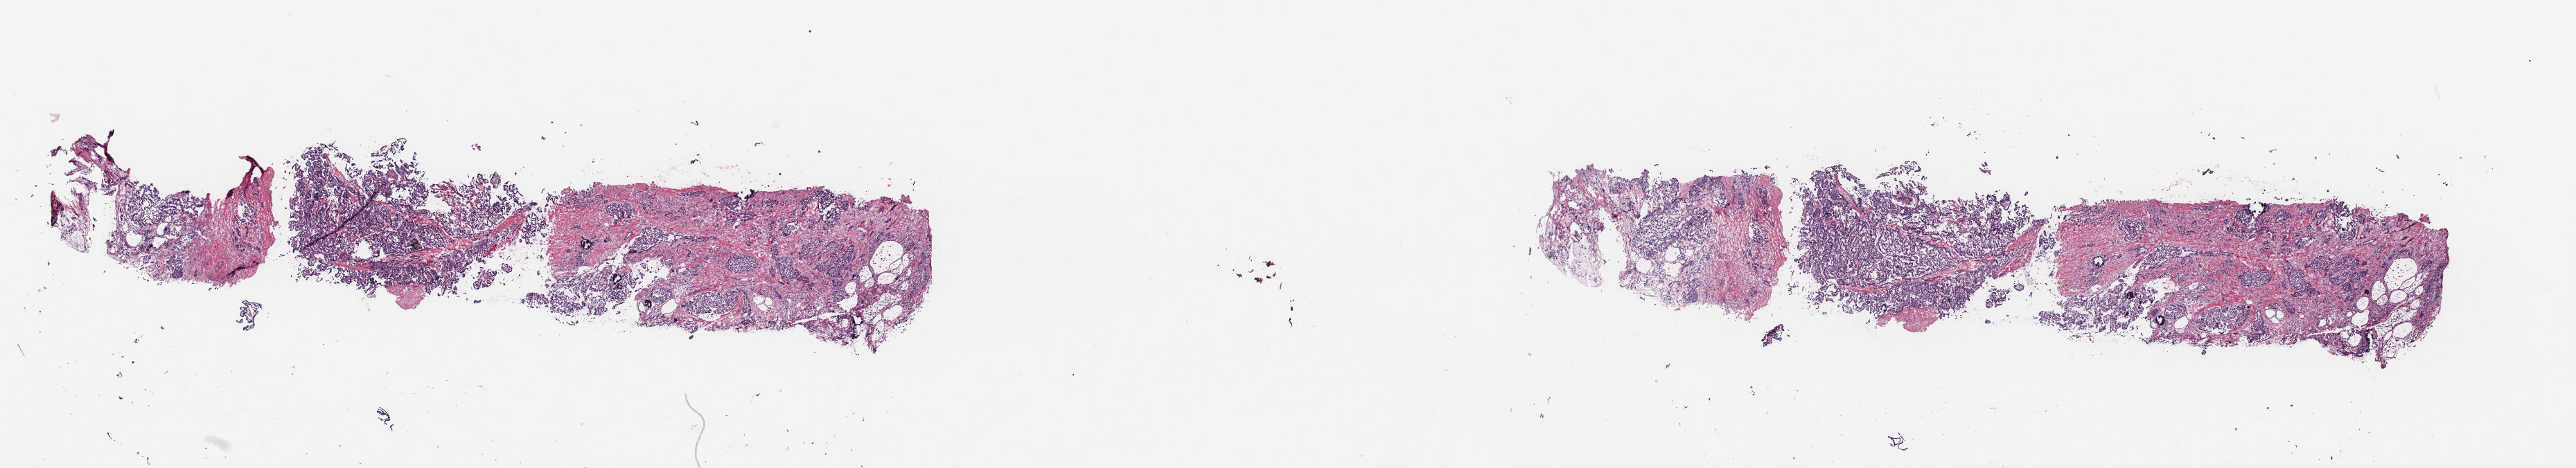
Digitized H&E-stained tissue section (whole slide) — whole scanned area (about 29.2 x 5.3 mm, slide scanned at 40x) shown as a low-resolution overview, frozen section from the top of the tissue portion, thyroid, primary tumour sample. Patient: male, age at initial diagnosis 32 years. Slide review estimates, as recorded: tumour cells 50%, tumour nuclei 100%, normal cells 0%, stromal cells 50%, necrosis 0%. Infiltration values recorded for this section: lymphocyte infiltration 2%, monocyte infiltration 1%, neutrophil infiltration 1%.
AJCC pathologic stage: I (7th edition). Pathologic diagnosis: Papillary adenocarcinoma, NOS (thyroid gland). TNM: T2 N1 M0.